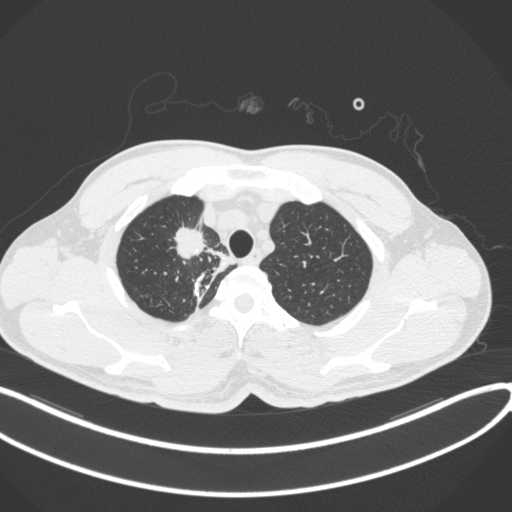
Chest CT, one axial slice; position 319 of 391 along the scan axis; 120 kVp; lung window (W 1500 / L -600 HU); 512 × 512 image matrix, field of view 400 × 400 mm. Patient: male, 48 years. Case-level facts recorded for this patient, not image findings: clinical TNM (as recorded): T1c N1 M1.
Structures marked on this image (rectangle marked by the reading radiologist):
- lung tumour (recorded histology: adenocarcinoma): bounding box (x1, y1, x2, y2) in pixels: (169, 221, 209, 261)